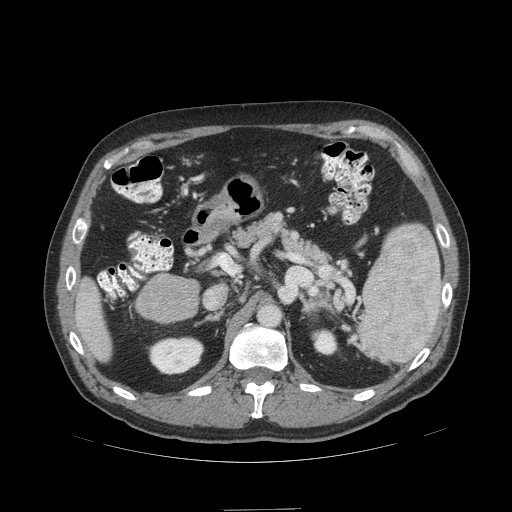
Contrast-enhanced abdominal CT (liver protocol), one axial slice; 140 kVp; soft-tissue window (W 400 / L 40 HU); 512 × 512 image matrix. From the clinical record (not read from this slice): diagnosis: hepatocellular carcinoma (patient treated with transarterial chemoembolisation; whether this scan precedes or follows treatment is not stated here); TNM stage (as recorded): Stage-I; Child-Pugh class: A; tumour differentiation: no biopsy; tumour nodularity: uninodular.
Outlined on this slice (semi-automatic segmentation, software-assisted and operator-edited):
- liver parenchyma outside the tumour (the mass and vessels are separate outlines, so this box may not span the whole liver): bounding box <74,276,112,360> (left, top, right, bottom; pixels)